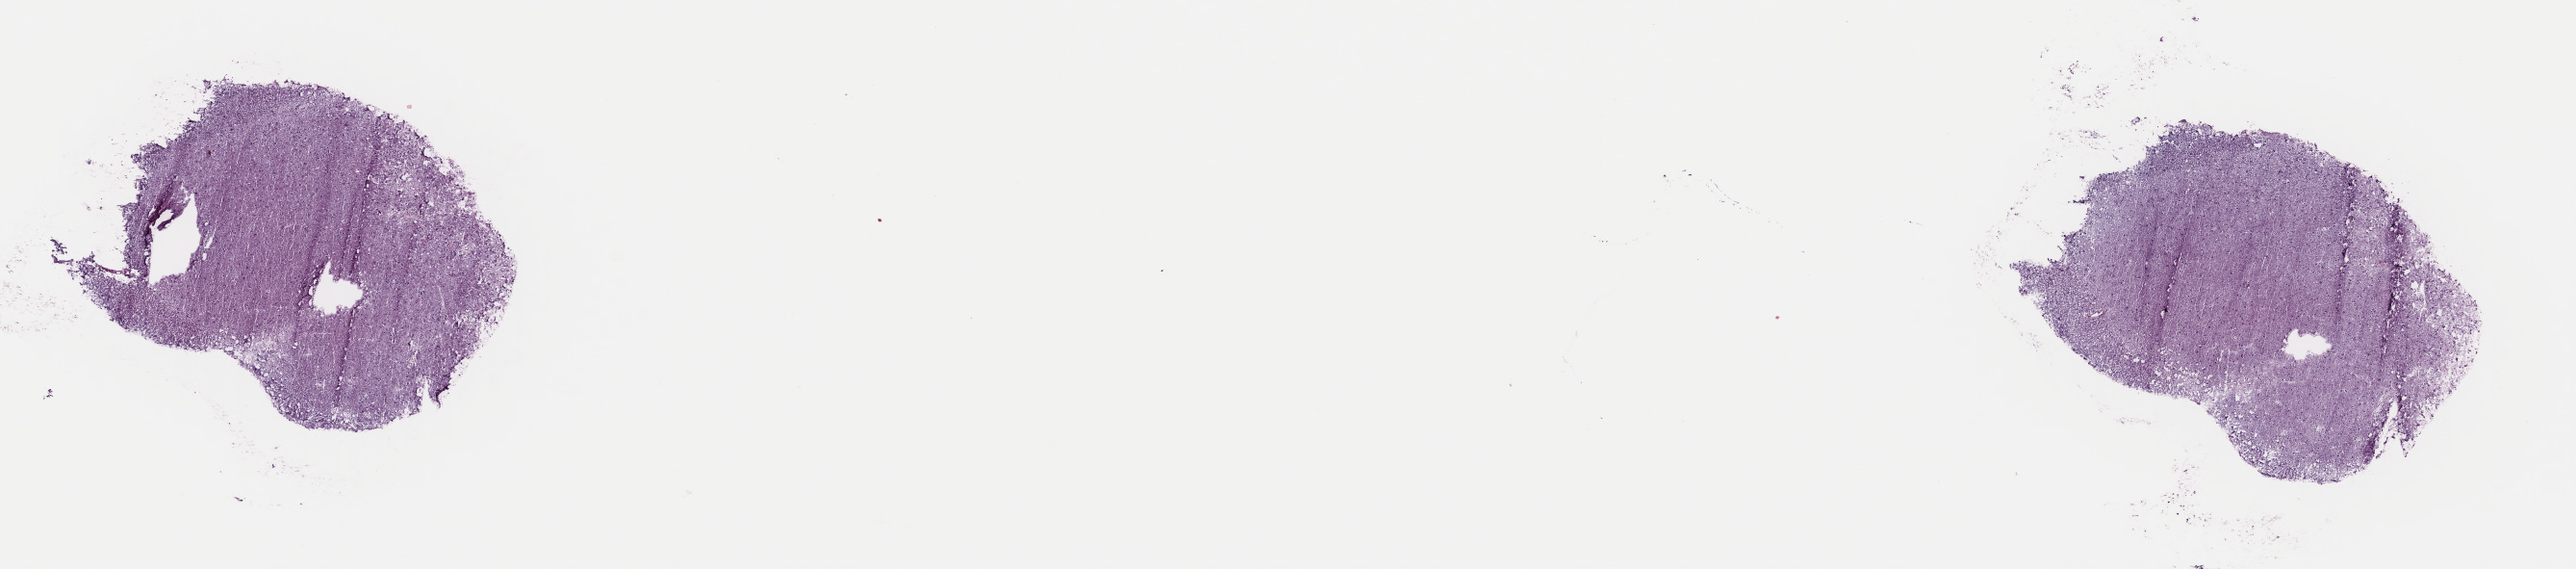
Digitized Hematoxylin and eosin (H&E) stained tissue section (whole slide), shown as a low-resolution overview of the whole scanned area (about 21.1 x 4.7 mm, from a 40x scan). Frozen section from the top of the tissue portion. Brain, primary tumour sample. Male patient; age at initial diagnosis 28 years.
Histologic diagnosis: Astrocytoma, anaplastic (cerebrum).